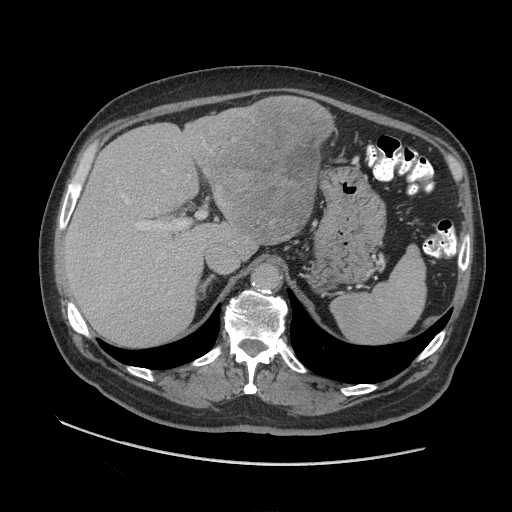
Contrast-enhanced abdominal CT (liver protocol), one axial slice; position 63 of 109 along the scan axis; soft-tissue window (W 400 / L 40 HU); 2.5 mm slice thickness; 512 × 512 image matrix, field of view 420 × 420 mm. From the clinical record (not read from this slice): diagnosis: hepatocellular carcinoma (patient treated with transarterial chemoembolisation; whether this scan precedes or follows treatment is not stated here); TNM stage (as recorded): Stage-I; Child-Pugh class: A; tumour nodularity: uninodular.
Annotated regions visible in this slice (semi-automatically segmented with operator editing):
- liver parenchyma outside the tumour (the mass and vessels are separate outlines, so this box may not span the whole liver): bounding box [x1, y1, x2, y2] px = [62, 106, 322, 346]
- mass: [203, 95, 336, 247]
- liver vessels: [98, 170, 181, 256]